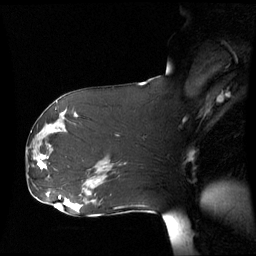
Breast MRI (dynamic contrast-enhanced), one sagittal slice; slice 32 of 60 in the series (ordered by position); dynamic contrast-enhanced series, image 2 of 3 at this slice position (ordered by acquisition); 1.5 T; TE 4.2 ms, TR 8.9 ms; 2.7 mm slice thickness; 256 × 256 image matrix, field of view 280 × 280 mm. Female patient, age 61 years. Case-level facts recorded for this patient, not image findings: setting: breast cancer imaged before/during neoadjuvant chemotherapy; receptor status: HR-positive, HER2-negative.
Structures marked on this image (semi-automatic segmentation, software-assisted and operator-edited):
- analysis volume of interest (the breast-tissue region the enhancement analysis was run in; not a lesion): box from (x=26, y=142) to (x=53, y=177) px
- tumour enhancement mask (voxels above the 70 % enhancement threshold inside the analysis volume of interest): (x=38, y=156)–(x=47, y=169)